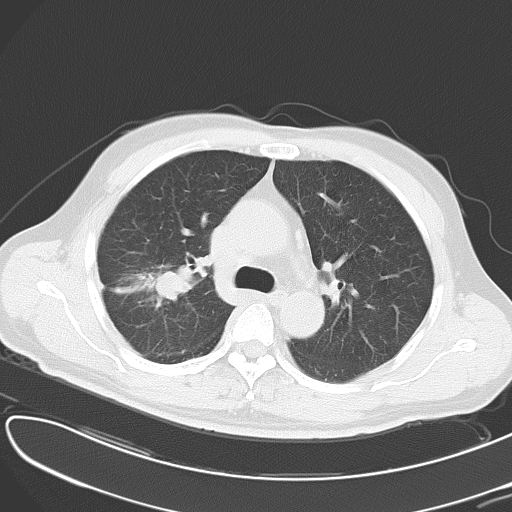
Chest CT, one axial slice; slice 33 of 49 in the series (ordered by position); 120 kVp; lung window (W 1500 / L -600 HU); 512 × 512 image matrix. Male patient, age 53 years. From the clinical record (not read from this slice): clinical TNM (as recorded): T2 N1 M0.
Structures marked on this image (rectangle marked by the reading radiologist):
- lung tumour (recorded histology: adenocarcinoma): bounding box [x1, y1, x2, y2] px = [108, 267, 195, 308]